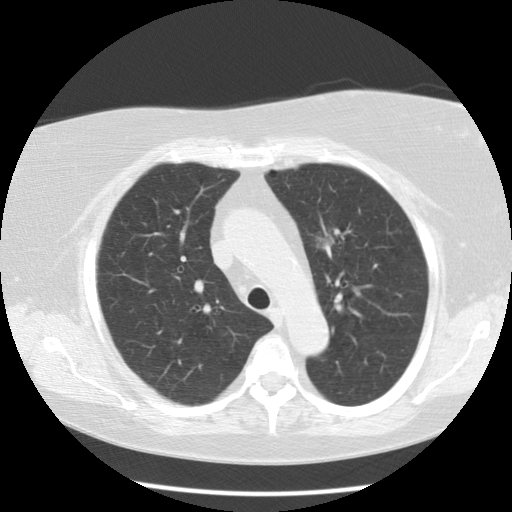
Low-dose screening chest CT, one axial slice; slice 83 of 109 in the series (ordered by position); 120 kVp; lung window (W 1500 / L -600 HU); 2.5 mm slice thickness; 512 × 512 image matrix, field of view 334 × 334 mm.
Structures marked on this image (outlined manually by an expert reader):
- lesion 1 (tumor, upper lobe of left lung): bounding box [x1, y1, x2, y2] px = [316, 235, 334, 248]